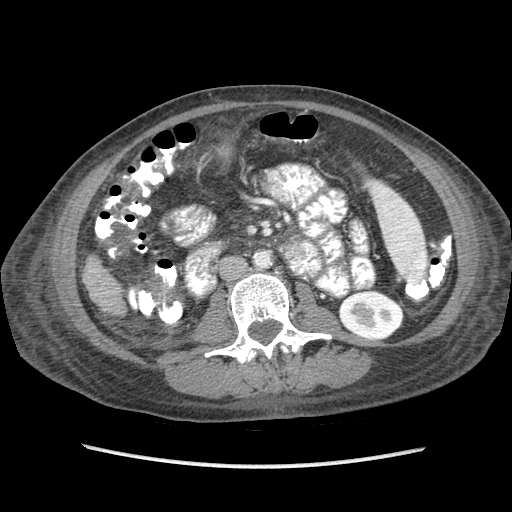
Contrast-enhanced abdominal CT (liver protocol), one axial slice; slice 17 of 87 in the series (ordered by position); reconstruction kernel STANDARD; soft-tissue window (W 400 / L 40 HU); 512 × 512 image matrix, field of view 340 × 340 mm. From the clinical record (not read from this slice): diagnosis: hepatocellular carcinoma (patient treated with transarterial chemoembolisation; whether this scan precedes or follows treatment is not stated here); TNM stage (as recorded): Stage-IIIB; Child-Pugh class: A; tumour differentiation: no biopsy; tumour nodularity: uninodular.
Annotated regions visible in this slice (semi-automatic segmentation, software-assisted and operator-edited):
- liver parenchyma outside the tumour (the mass and vessels are separate outlines, so this box may not span the whole liver): box from (x=84, y=256) to (x=124, y=312) px